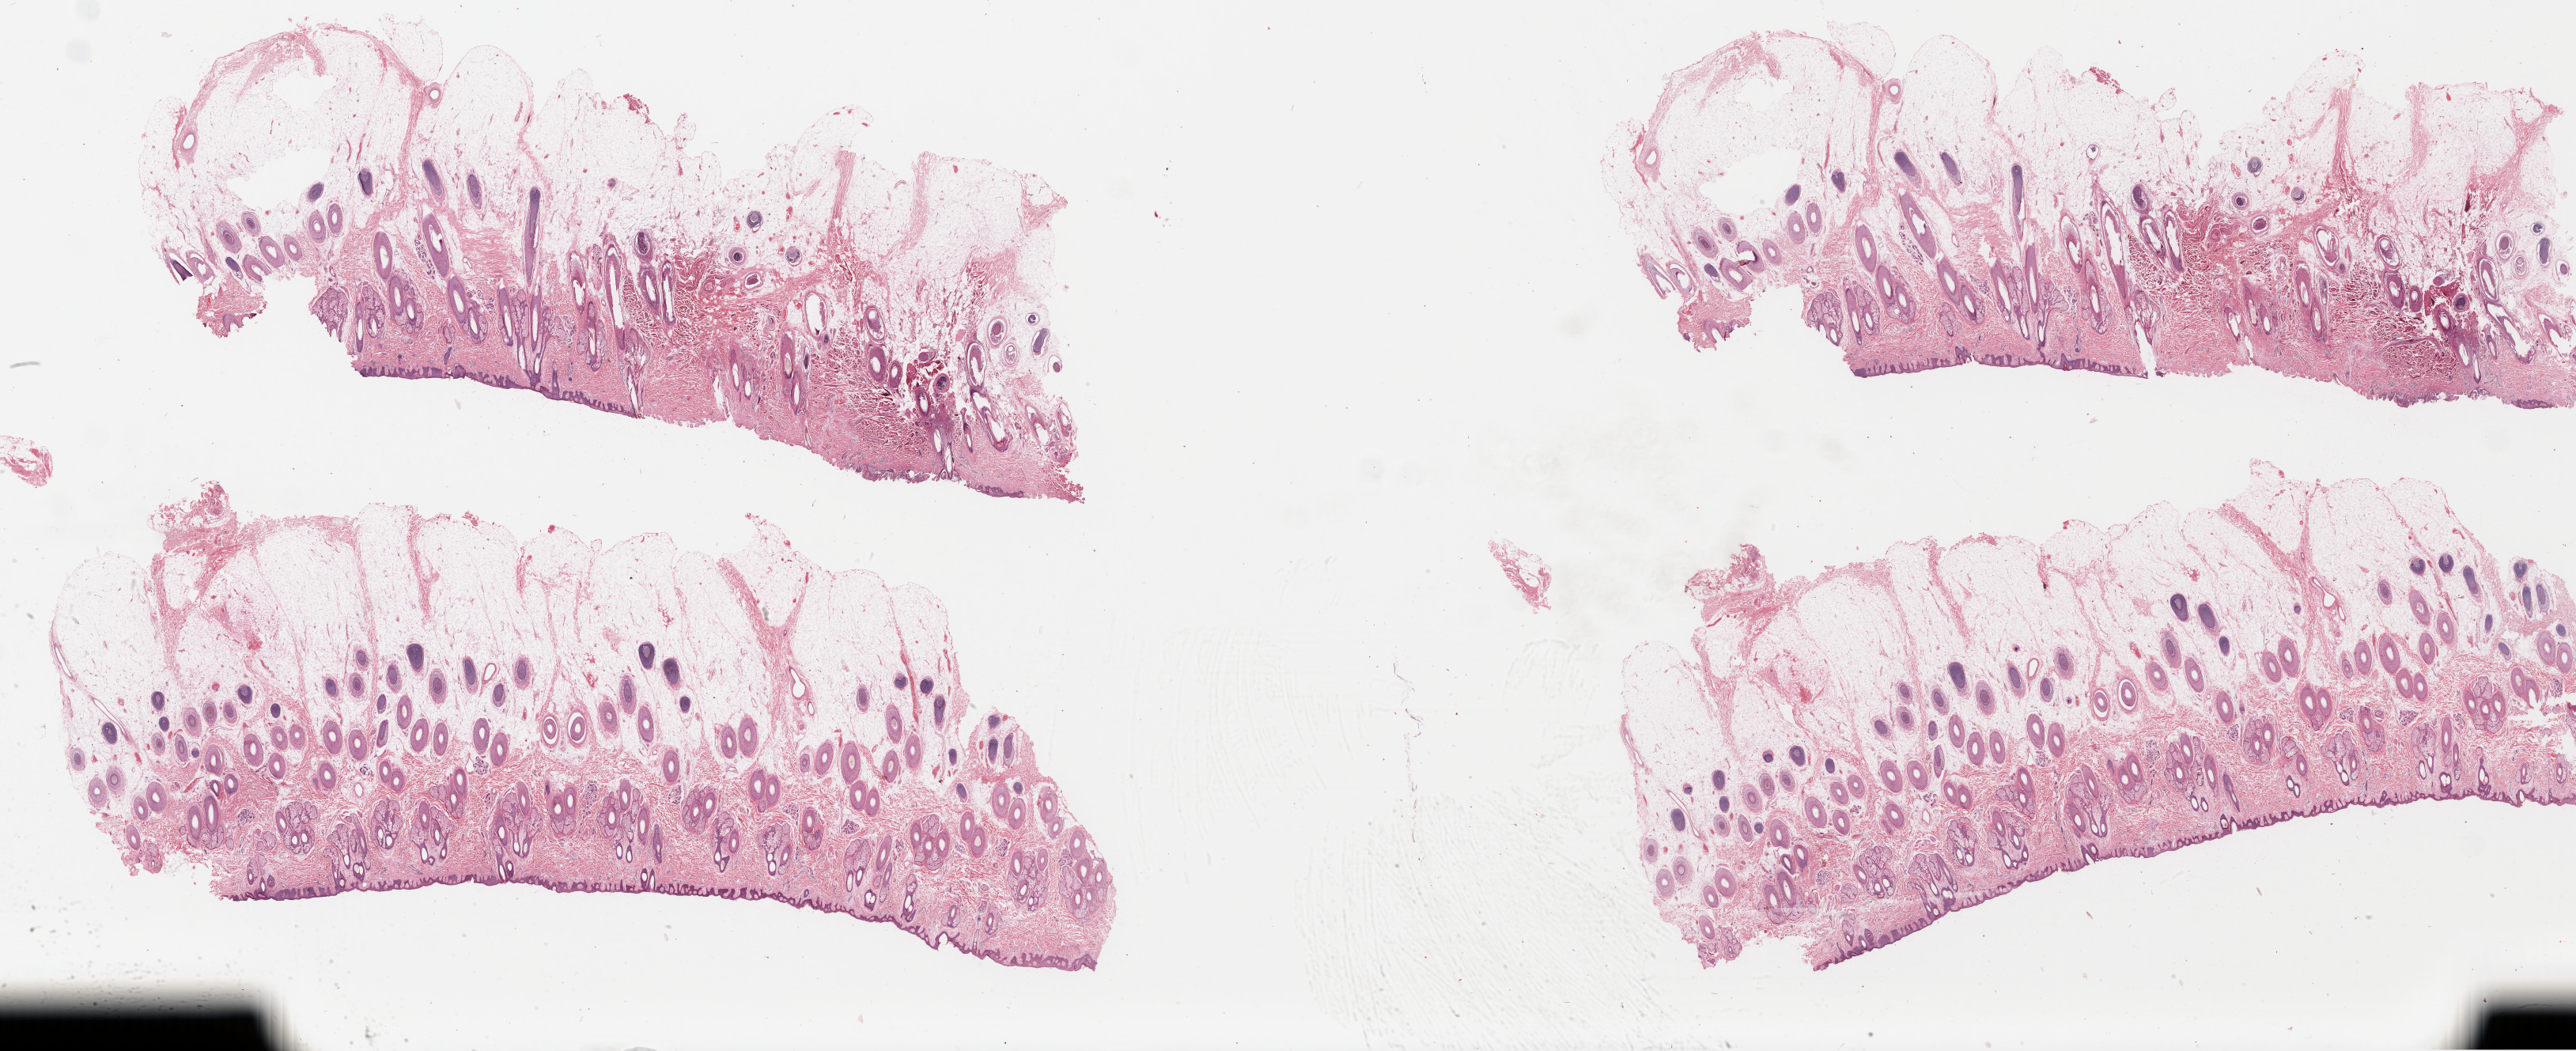
Digitized Hematoxylin and eosin (H&E) stained tissue section (whole slide) — low-resolution overview of the scanned area, about 51.2 x 20.9 mm. Formalin-fixed paraffin-embedded (FFPE) diagnostic section. Metastatic tumour sample. Patient: male, age at initial diagnosis 19 years.
* this section: metastatic tumour tissue
* patient diagnosis: Malignant melanoma, NOS